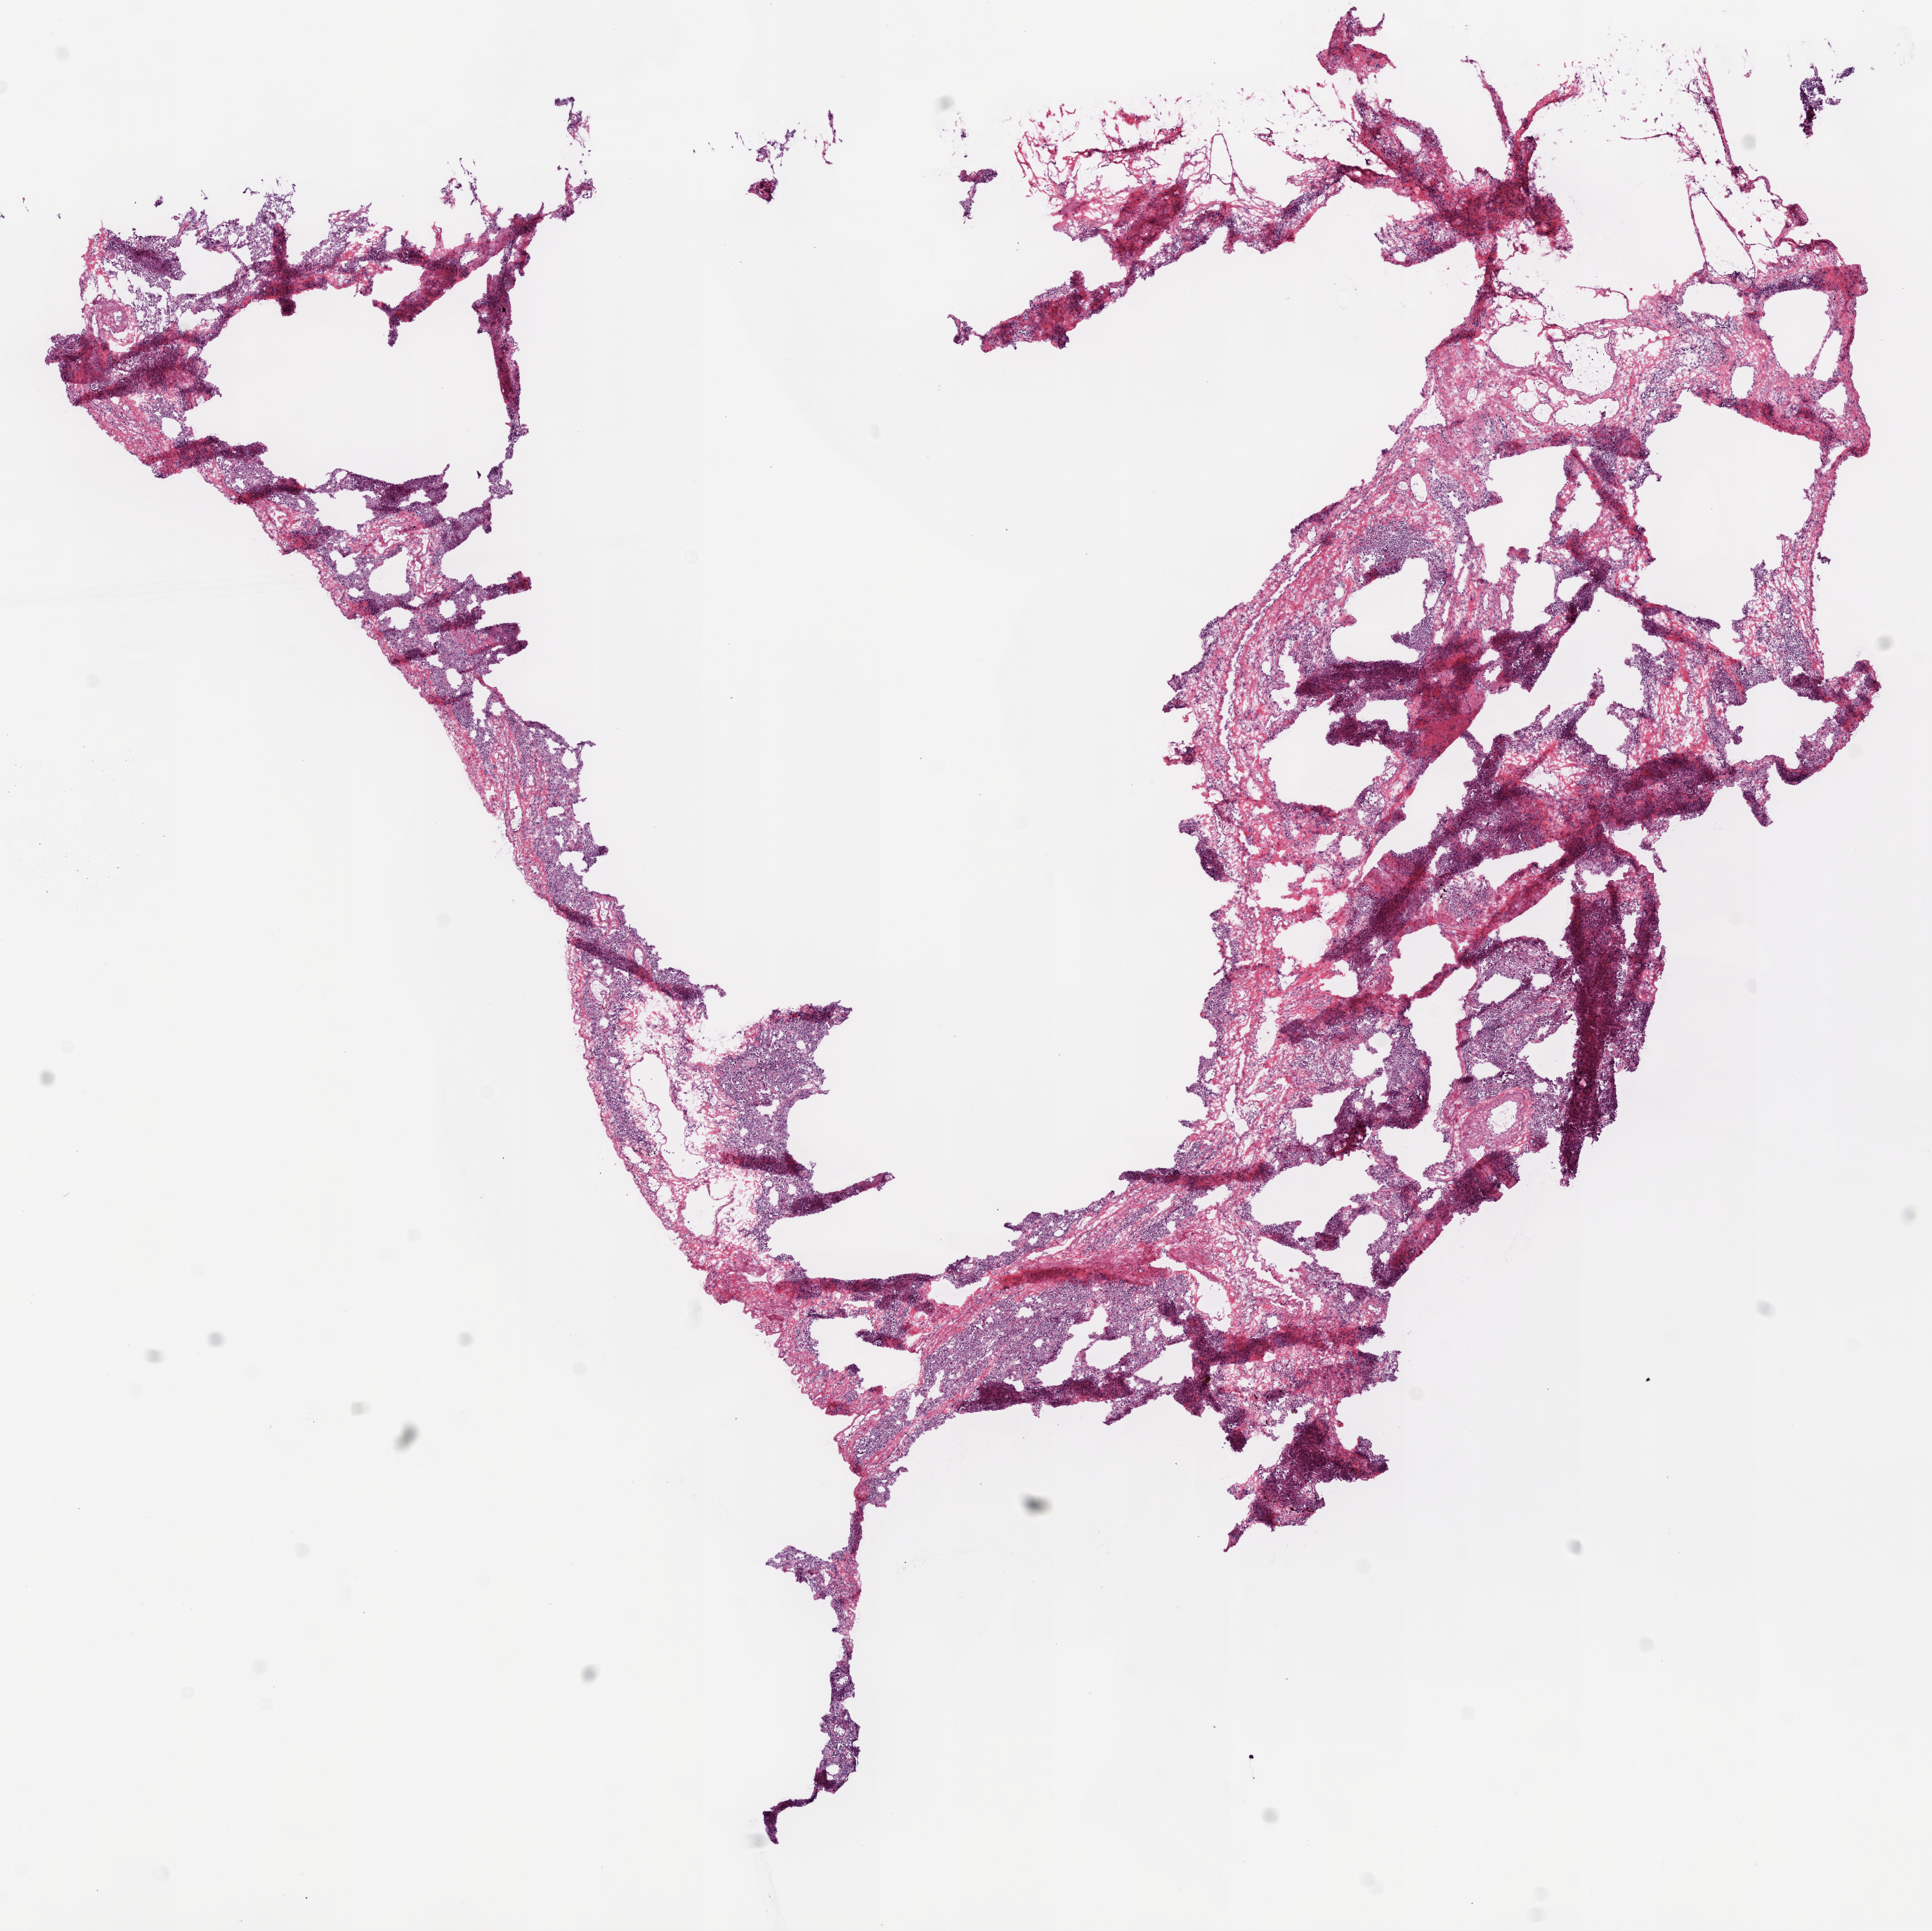
Digitized H&E tissue section (whole slide) — whole scanned area (about 11.0 x 11.0 mm, acquisition: 20x scan) shown as a low-resolution overview, frozen section from the top of the tissue portion, solid tissue normal (non-tumour tissue) sample from the lung. Male patient; age at initial diagnosis 69 years.
• this section: solid tissue normal sample (biorepository sample class)
• patient diagnosis: Squamous cell carcinoma, NOS (lower lobe, lung)